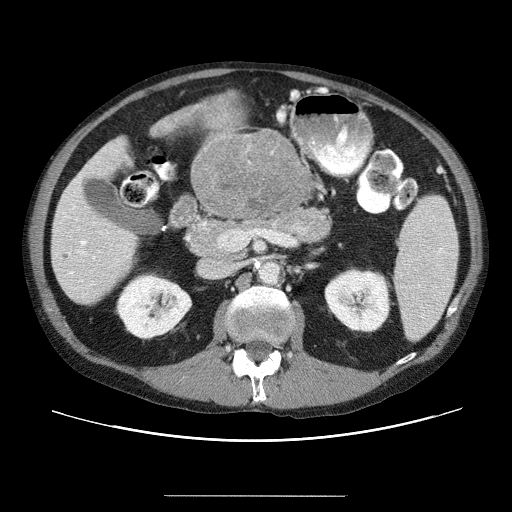
Contrast-enhanced abdominal CT (liver protocol), one axial slice. Position 12 of 69 along the scan axis. 120 kVp. Soft-tissue window (W 400 / L 40 HU). 512 × 512 image matrix, field of view 380 × 380 mm. Case-level facts recorded for this patient, not image findings: diagnosis: hepatocellular carcinoma (patient treated with transarterial chemoembolisation; whether this scan precedes or follows treatment is not stated here); TNM stage (as recorded): Stage-IVB; Child-Pugh class: B; tumour differentiation: poorly differentiated; tumour nodularity: multinodular.
Structures marked on this image (semi-automatically segmented with operator editing):
- liver parenchyma outside the tumour (the mass and vessels are separate outlines, so this box may not span the whole liver): bounding box <50,134,296,300> (left, top, right, bottom; pixels)
- mass: <191,134,310,224>
- liver vessels: <57,152,129,289>